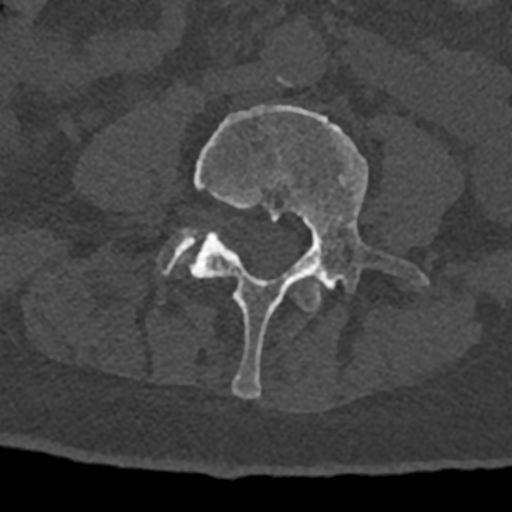
CT including the spine, one axial slice. Reconstruction kernel Br40s/3. 120 kVp. Bone window (W 1800 / L 400 HU). 0.5 mm slice thickness. 512 × 512 image matrix. Patient: male, 74 years. Case-level facts recorded for this patient, not image findings: primary cancer: renal; vertebrae with lytic lesions (as recorded): T10, L1, L2, L3, L4, L5.
Outlined on this slice (semi-automatic segmentation, software-assisted and operator-edited):
- L3 vertebra: box from (x=296, y=275) to (x=322, y=311) px
- L4 vertebra: (x=189, y=105)–(x=429, y=399)
- L5 vertebra: (x=160, y=227)–(x=198, y=275)